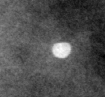
Region of interest cut from a scanned film mammogram (one marked finding); right breast; CC view; BI-RADS breast density category 3 (scale 1–4).
Marked abnormality: calcifications, morphology round and regular / lucent center; BI-RADS assessment category 2; subtlety rating 5 on a 1 (subtle) to 5 (obvious) scale; benign; no additional work-up was recommended (benign without callback).